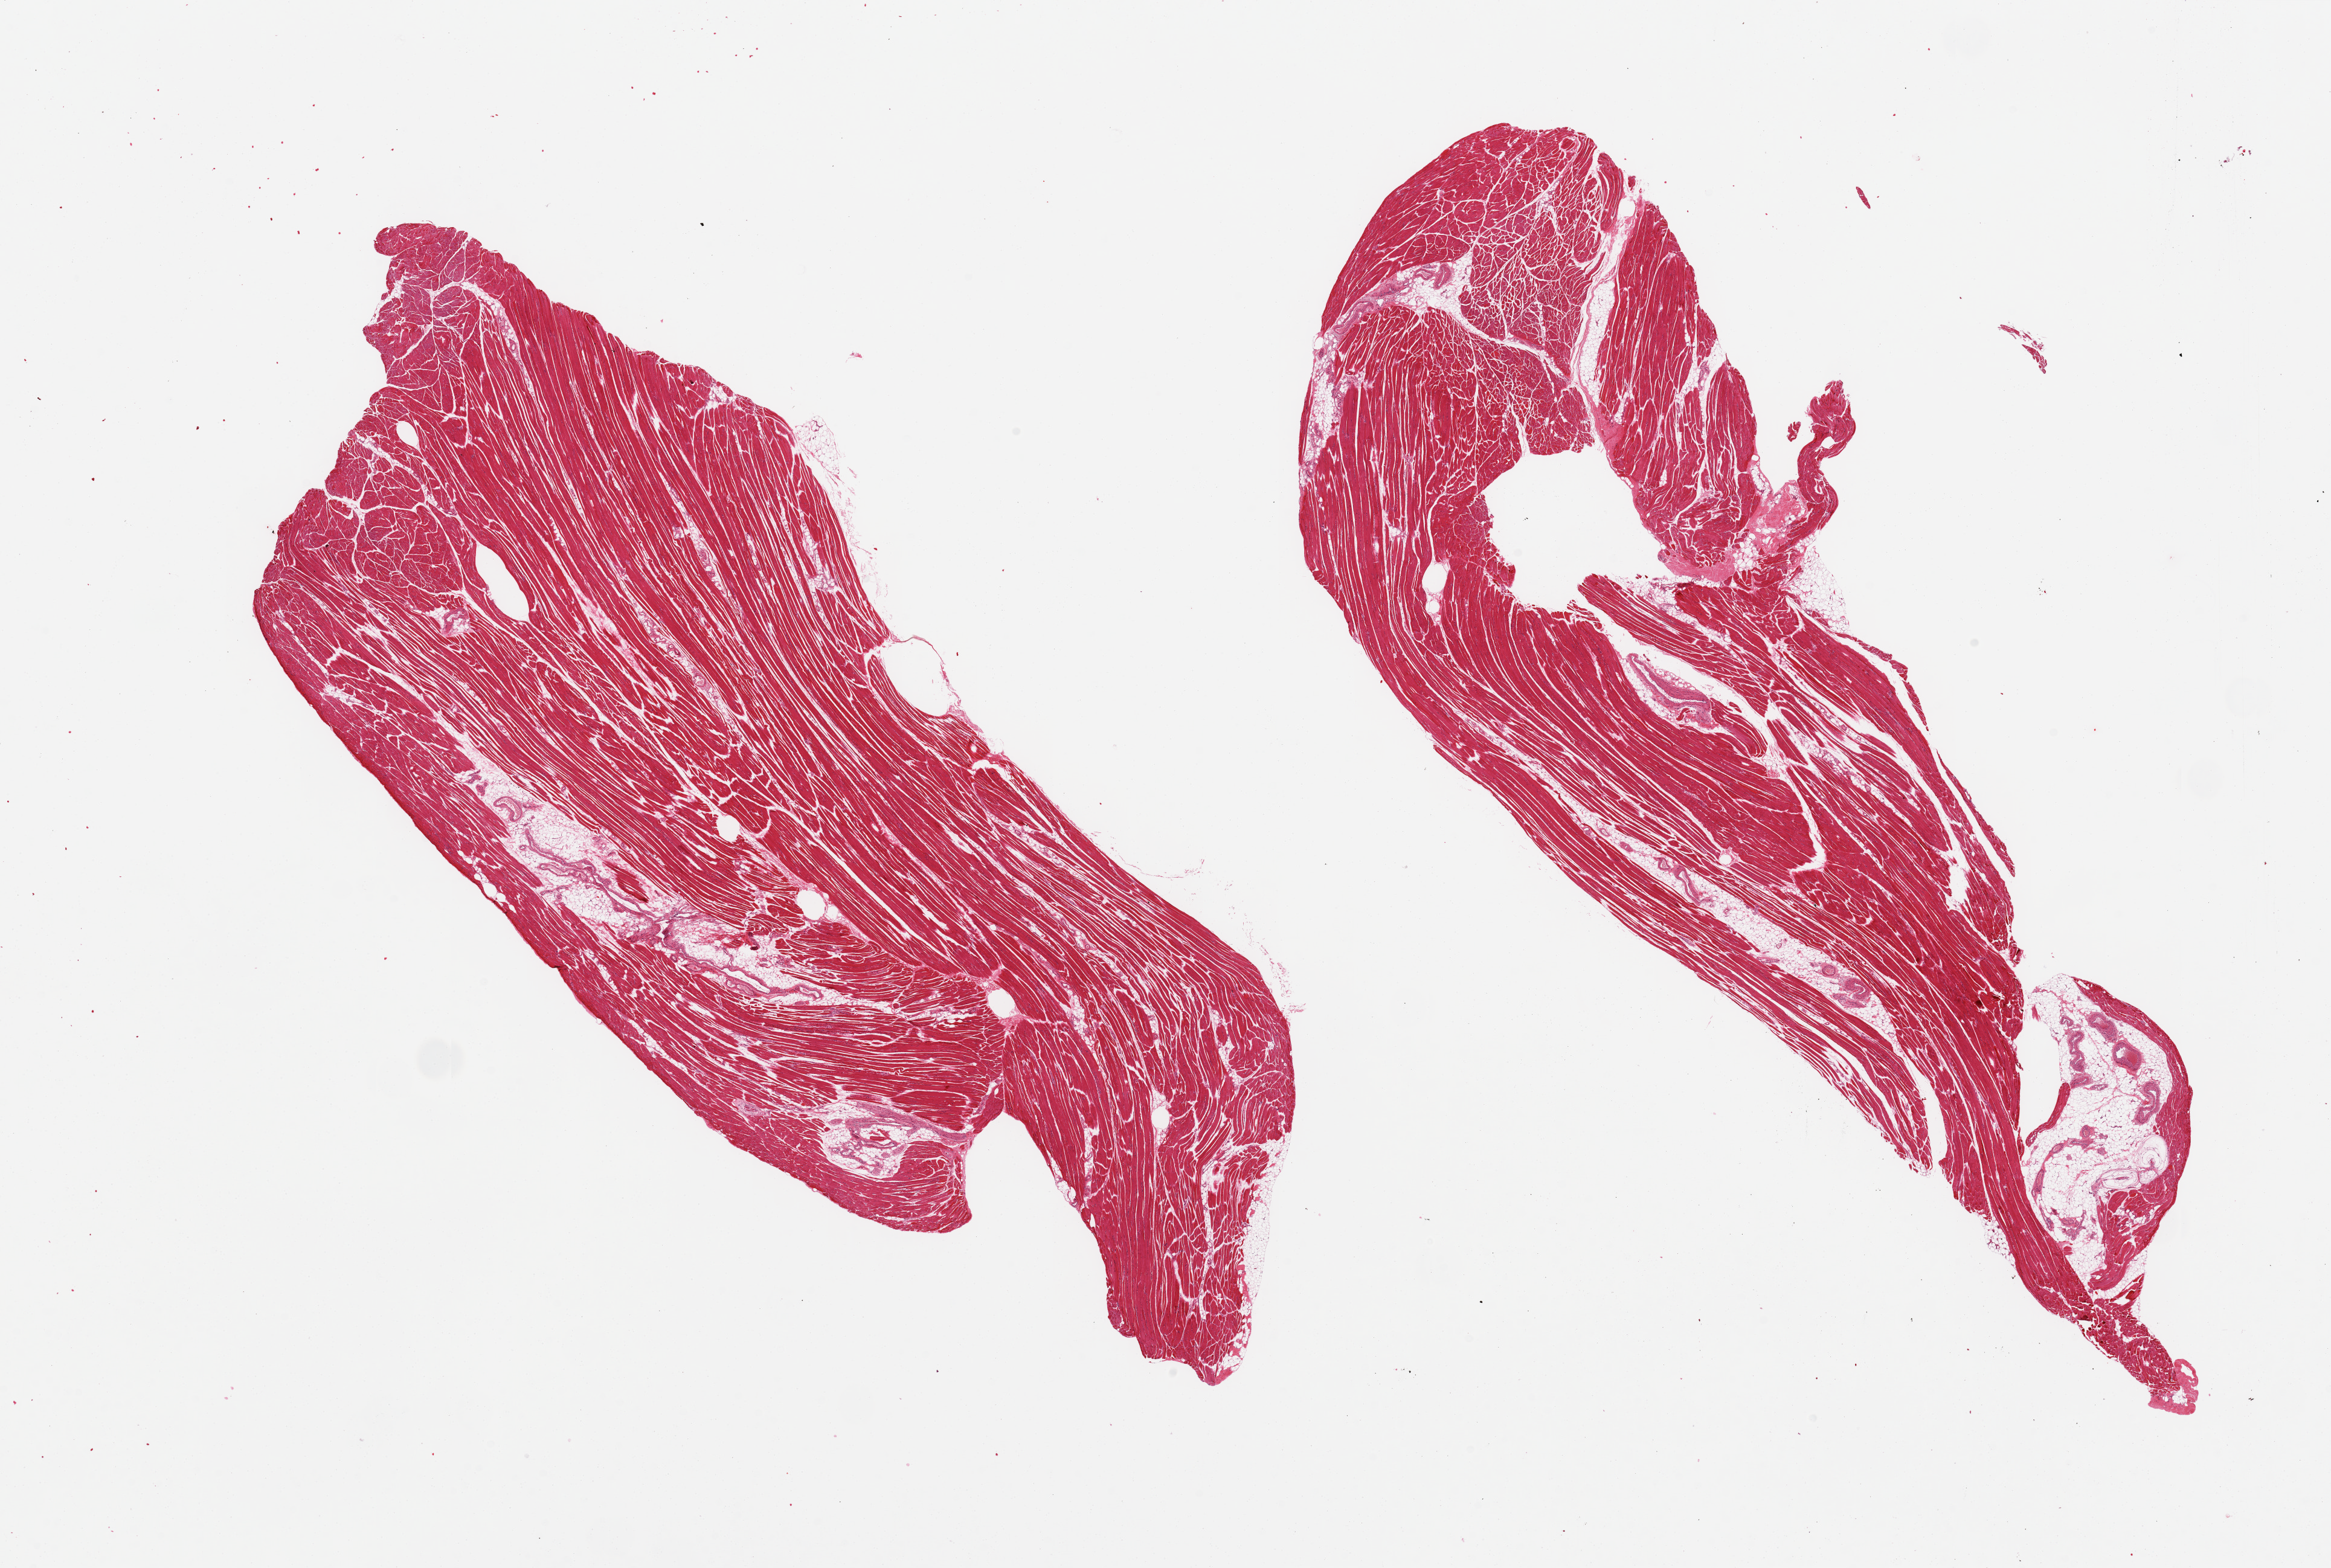
Whole-slide image, haematoxylin and eosin stain — a low-resolution overview of the entire scanned area, about 30.5 x 20.5 mm; PAXgene-fixed, paraffin-embedded tissue; target tissue: skeletal muscle; donor tissue sample. Donor: female.
- reviewer comment on this tissue sample: 2 pieces, 10-15% interstitial fat